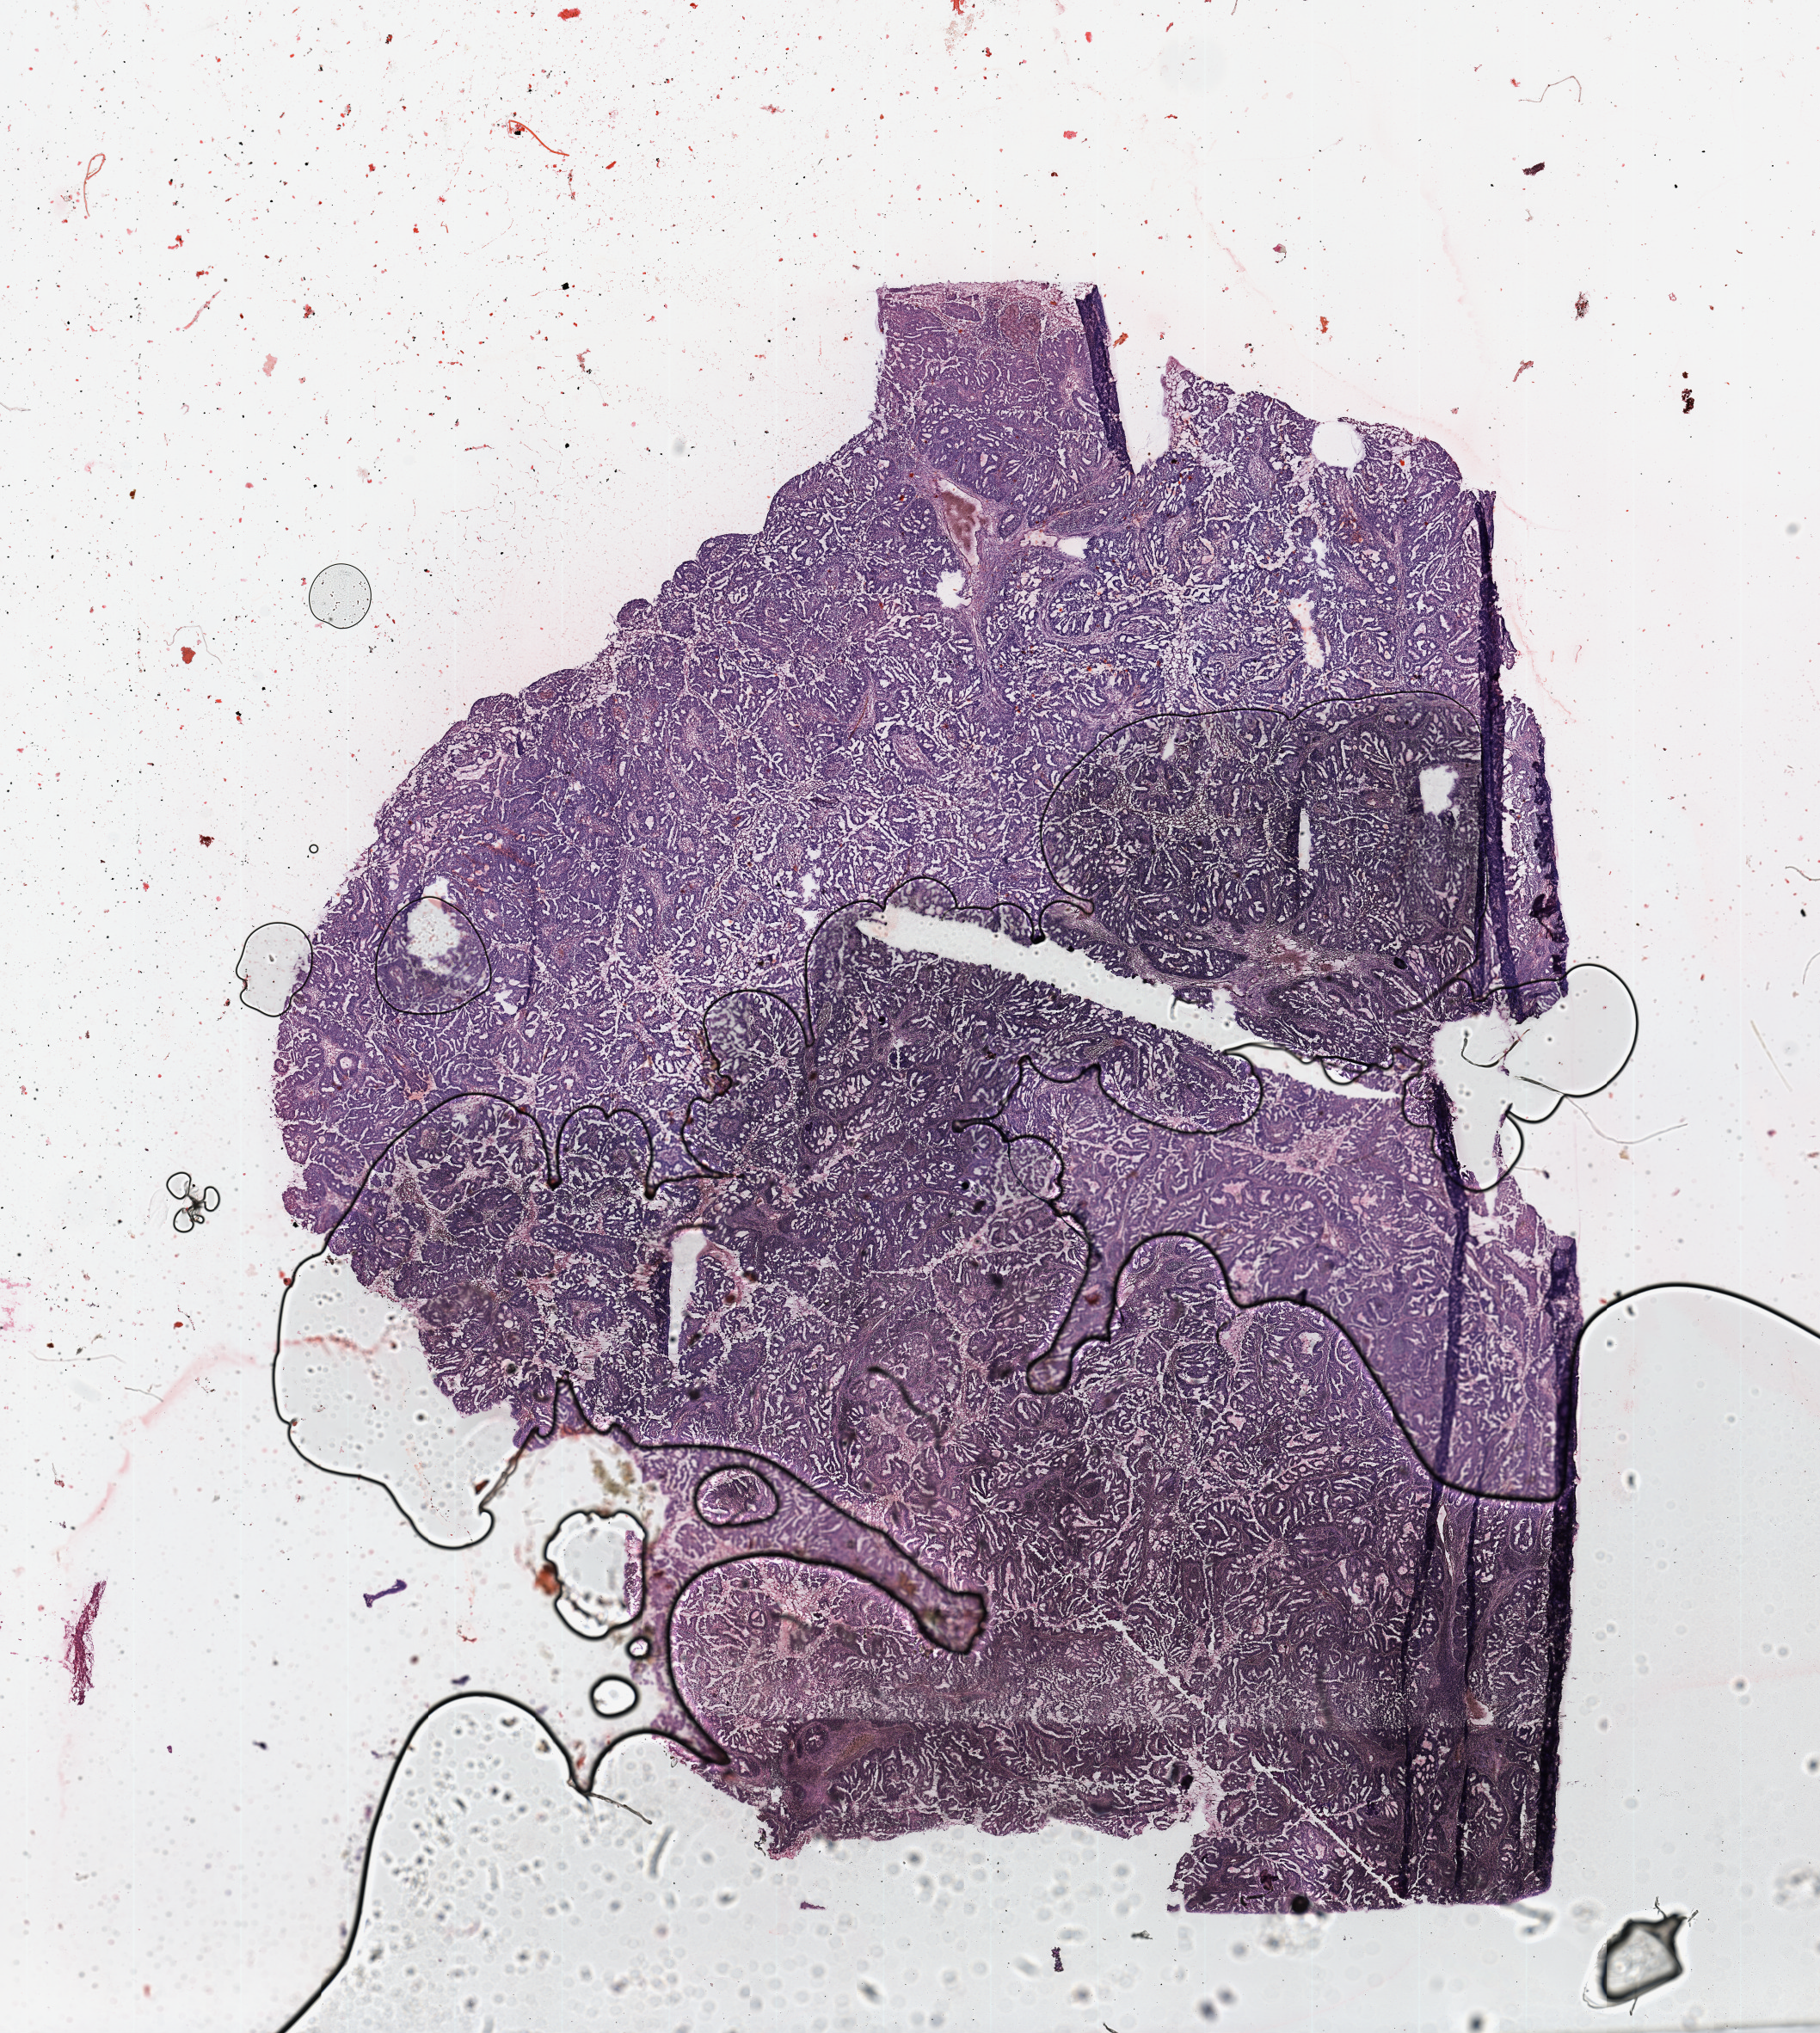
Whole-slide histology image, Hematoxylin and eosin (H&E) stained — a low-resolution overview of the entire scanned area, about 16.7 x 18.7 mm (acquisition: 20x scan); uterus, tumour tissue. Female, 59 y/o. Histologic grade: G2 (moderately differentiated).
Histologic diagnosis: Endometrioid adenocarcinoma, NOS. AJCC pathologic stage: I.